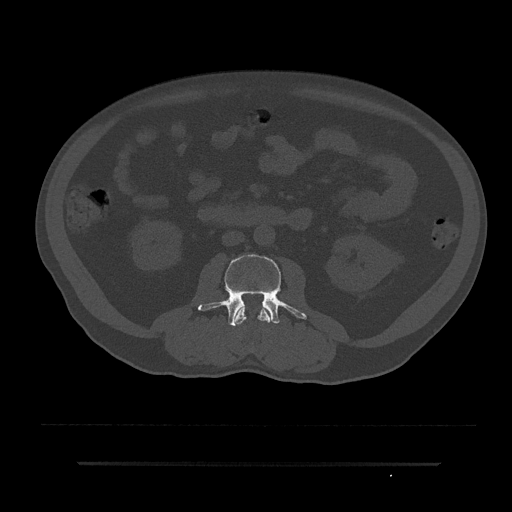
CT including the spine, one axial slice; slice 24 of 797 in the series (ordered by position); bone window (W 1800 / L 400 HU); 0.5 mm slice thickness; 512 × 512 image matrix, field of view 464 × 464 mm. Male patient, age 59 years. Case-level facts recorded for this patient, not image findings: primary cancer: bile ducts.
Annotated regions visible in this slice (semi-automatic segmentation, software-assisted and operator-edited):
- L2 vertebra: bounding box [x1, y1, x2, y2] px = [234, 306, 272, 325]
- L3 vertebra: [198, 254, 307, 326]